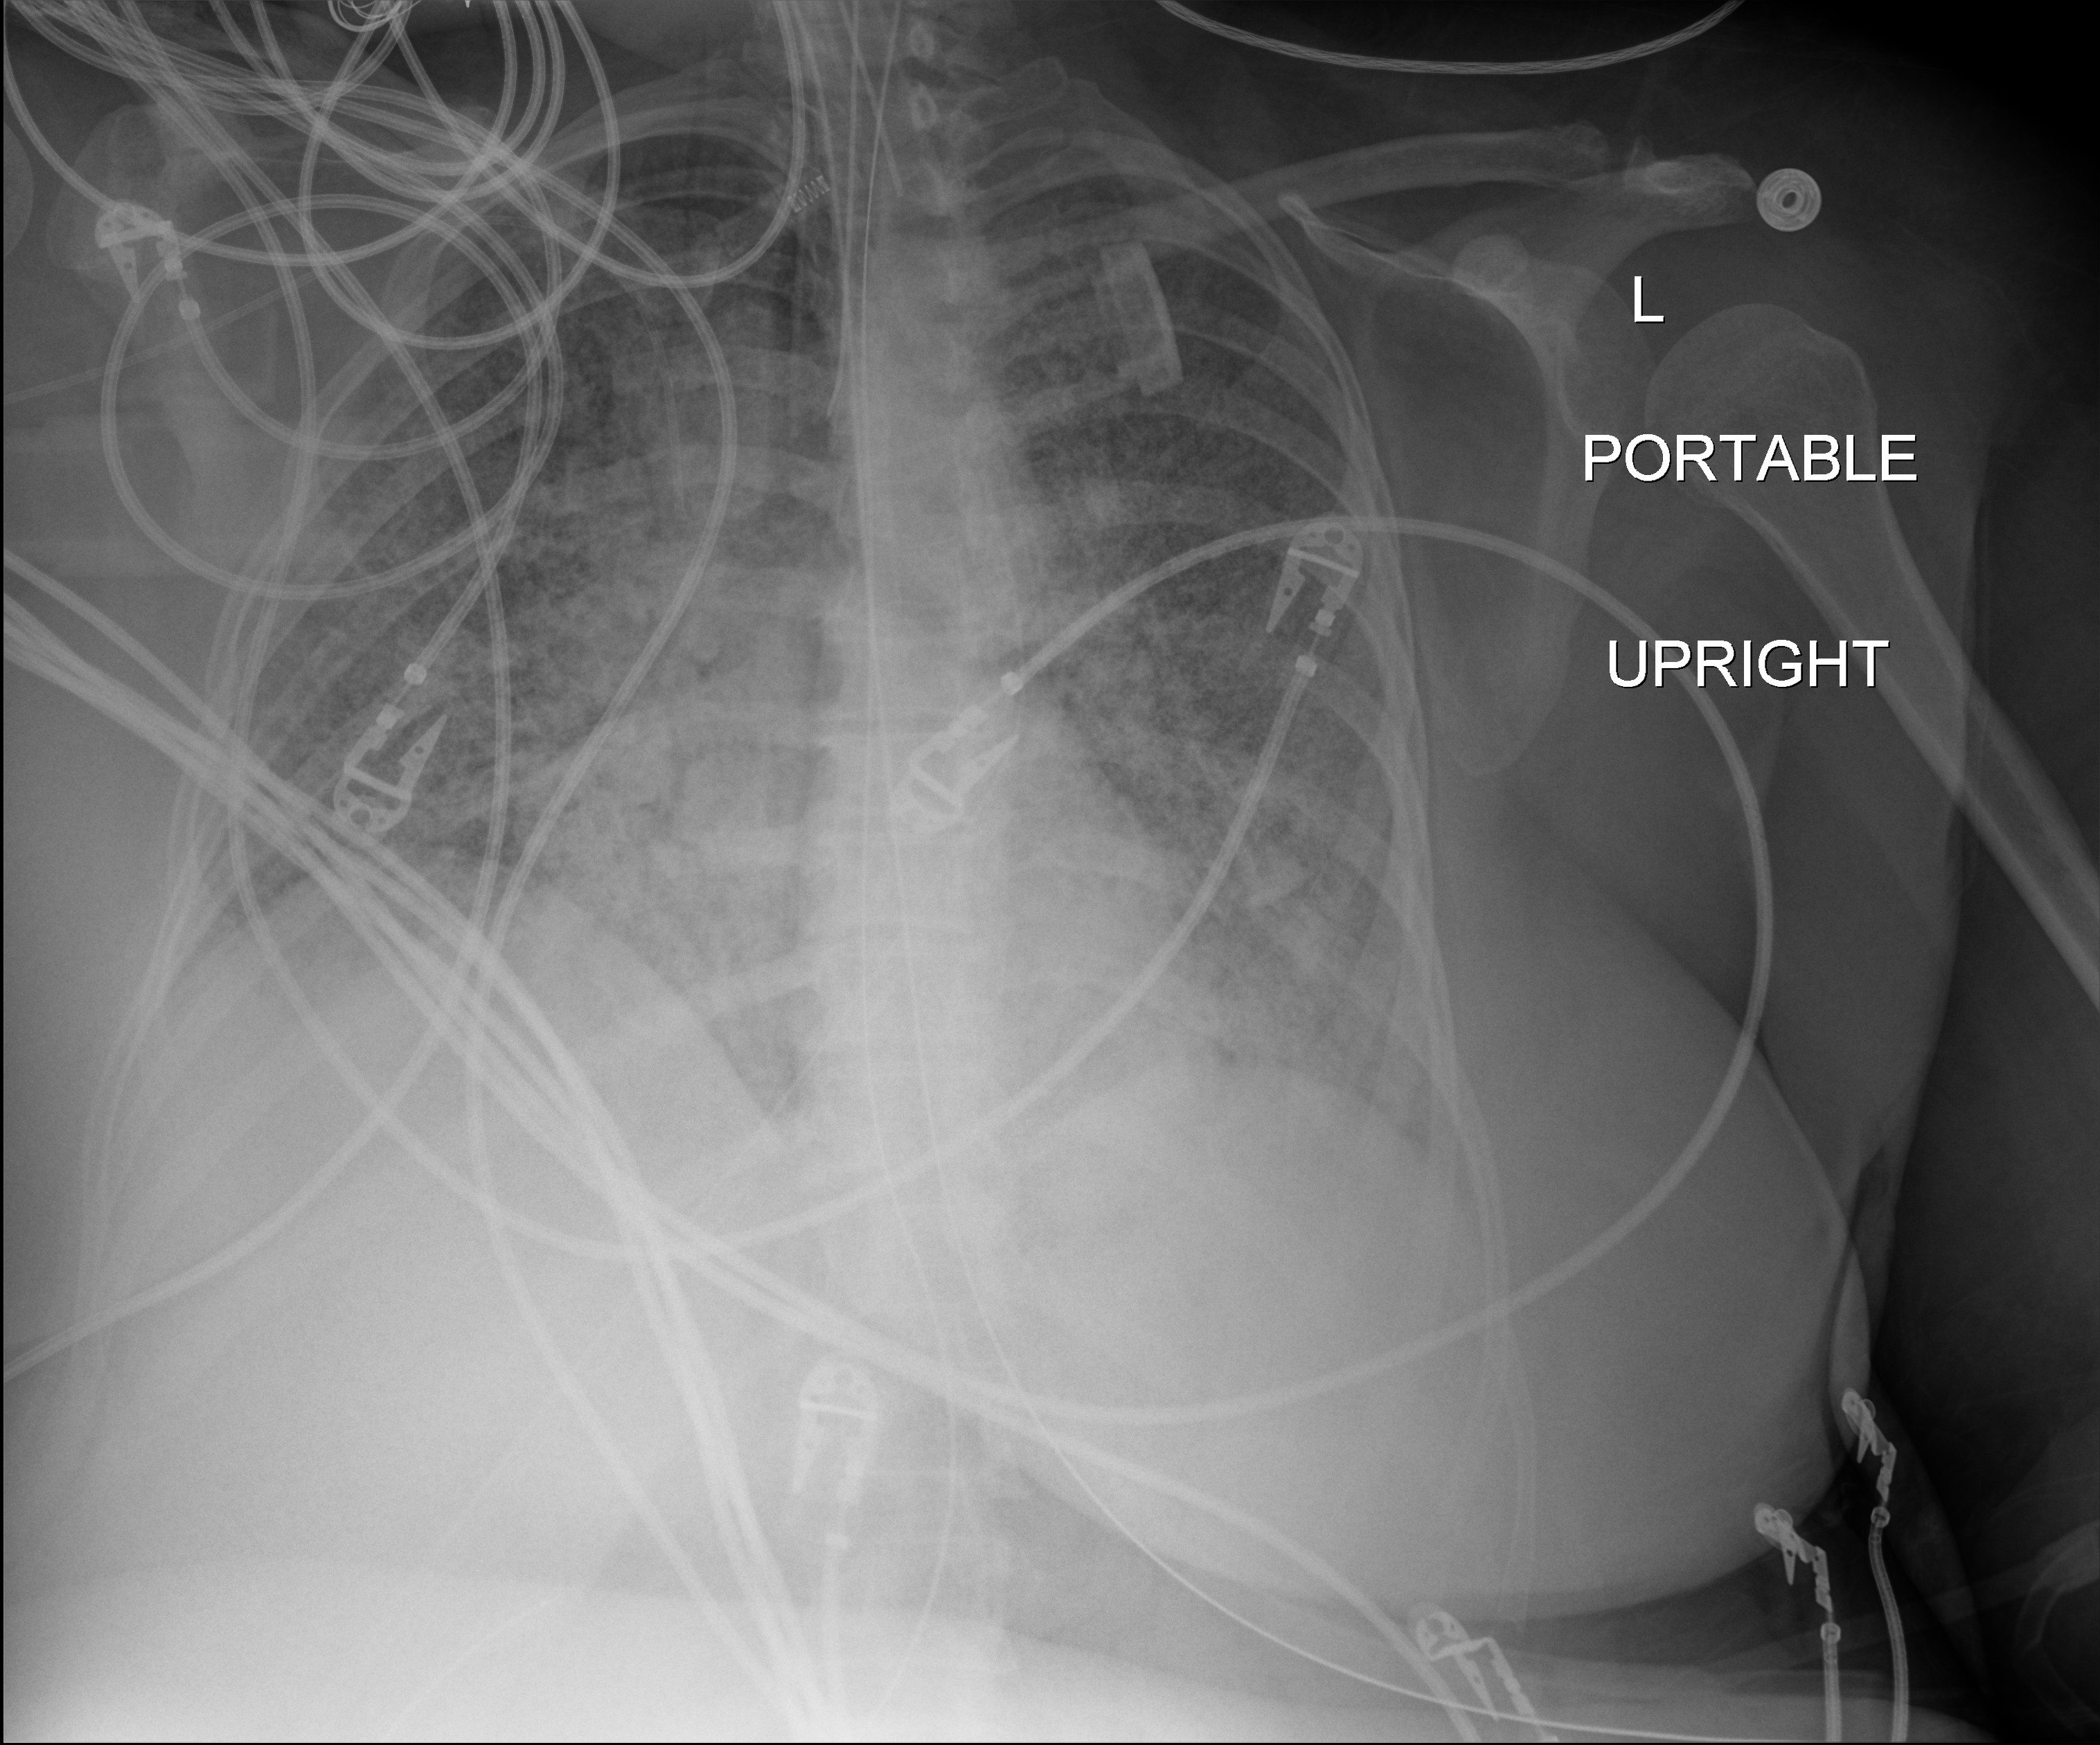
Portable chest radiograph; anteroposterior (AP) projection. Patient hospitalised with COVID-19; female, aged 18–59 years.
Admission-level facts for this patient (not findings on this image; timing relative to this image not recorded): other chronic lung disease (admission record): no.